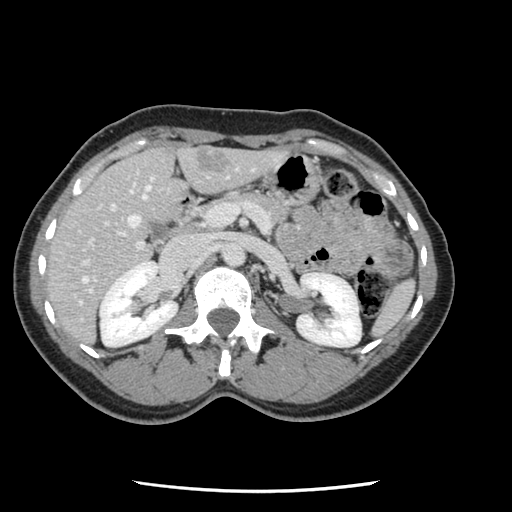
Contrast-enhanced abdominal CT, one axial slice. Position 58 of 134 along the scan axis. Intravenous contrast given. Soft-tissue window (W 400 / L 40 HU). 512 × 512 image matrix. Female patient, age 43 years. Case-level facts recorded for this patient, not image findings: diagnosis: colorectal cancer liver metastases, imaged before liver resection; multiple liver metastases: yes; largest metastasis: 3.4 cm; disease in both lobes: yes.
Structures marked on this image (expert manual segmentation):
- hepatic veins: bounding box <82,177,153,283> (left, top, right, bottom; pixels)
- liver: <45,146,286,346>
- planned liver remnant (the part of the liver to remain after resection): <46,146,183,321>
- portal vein (with intrahepatic branches): <82,169,271,294>
- liver metastasis: <196,151,229,173>